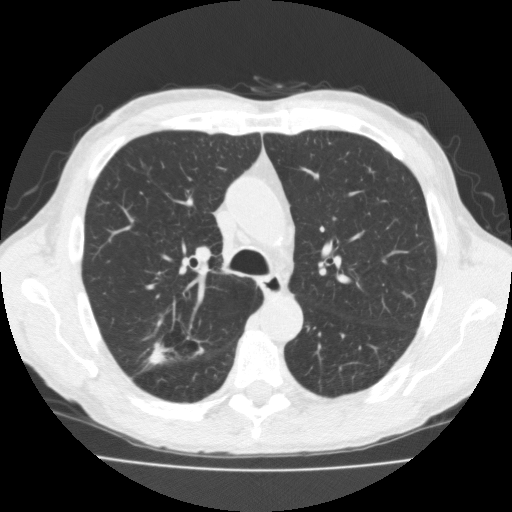
Low-dose screening chest CT, one axial slice; position 120 of 181 along the scan axis; 120 kVp; lung window (W 1500 / L -600 HU); 512 × 512 image matrix, field of view 350 × 350 mm.
Annotated regions visible in this slice (manually delineated by an expert):
- lesion 1 (tumor, upper lobe of right lung): bounding box <149,343,168,364> (left, top, right, bottom; pixels)